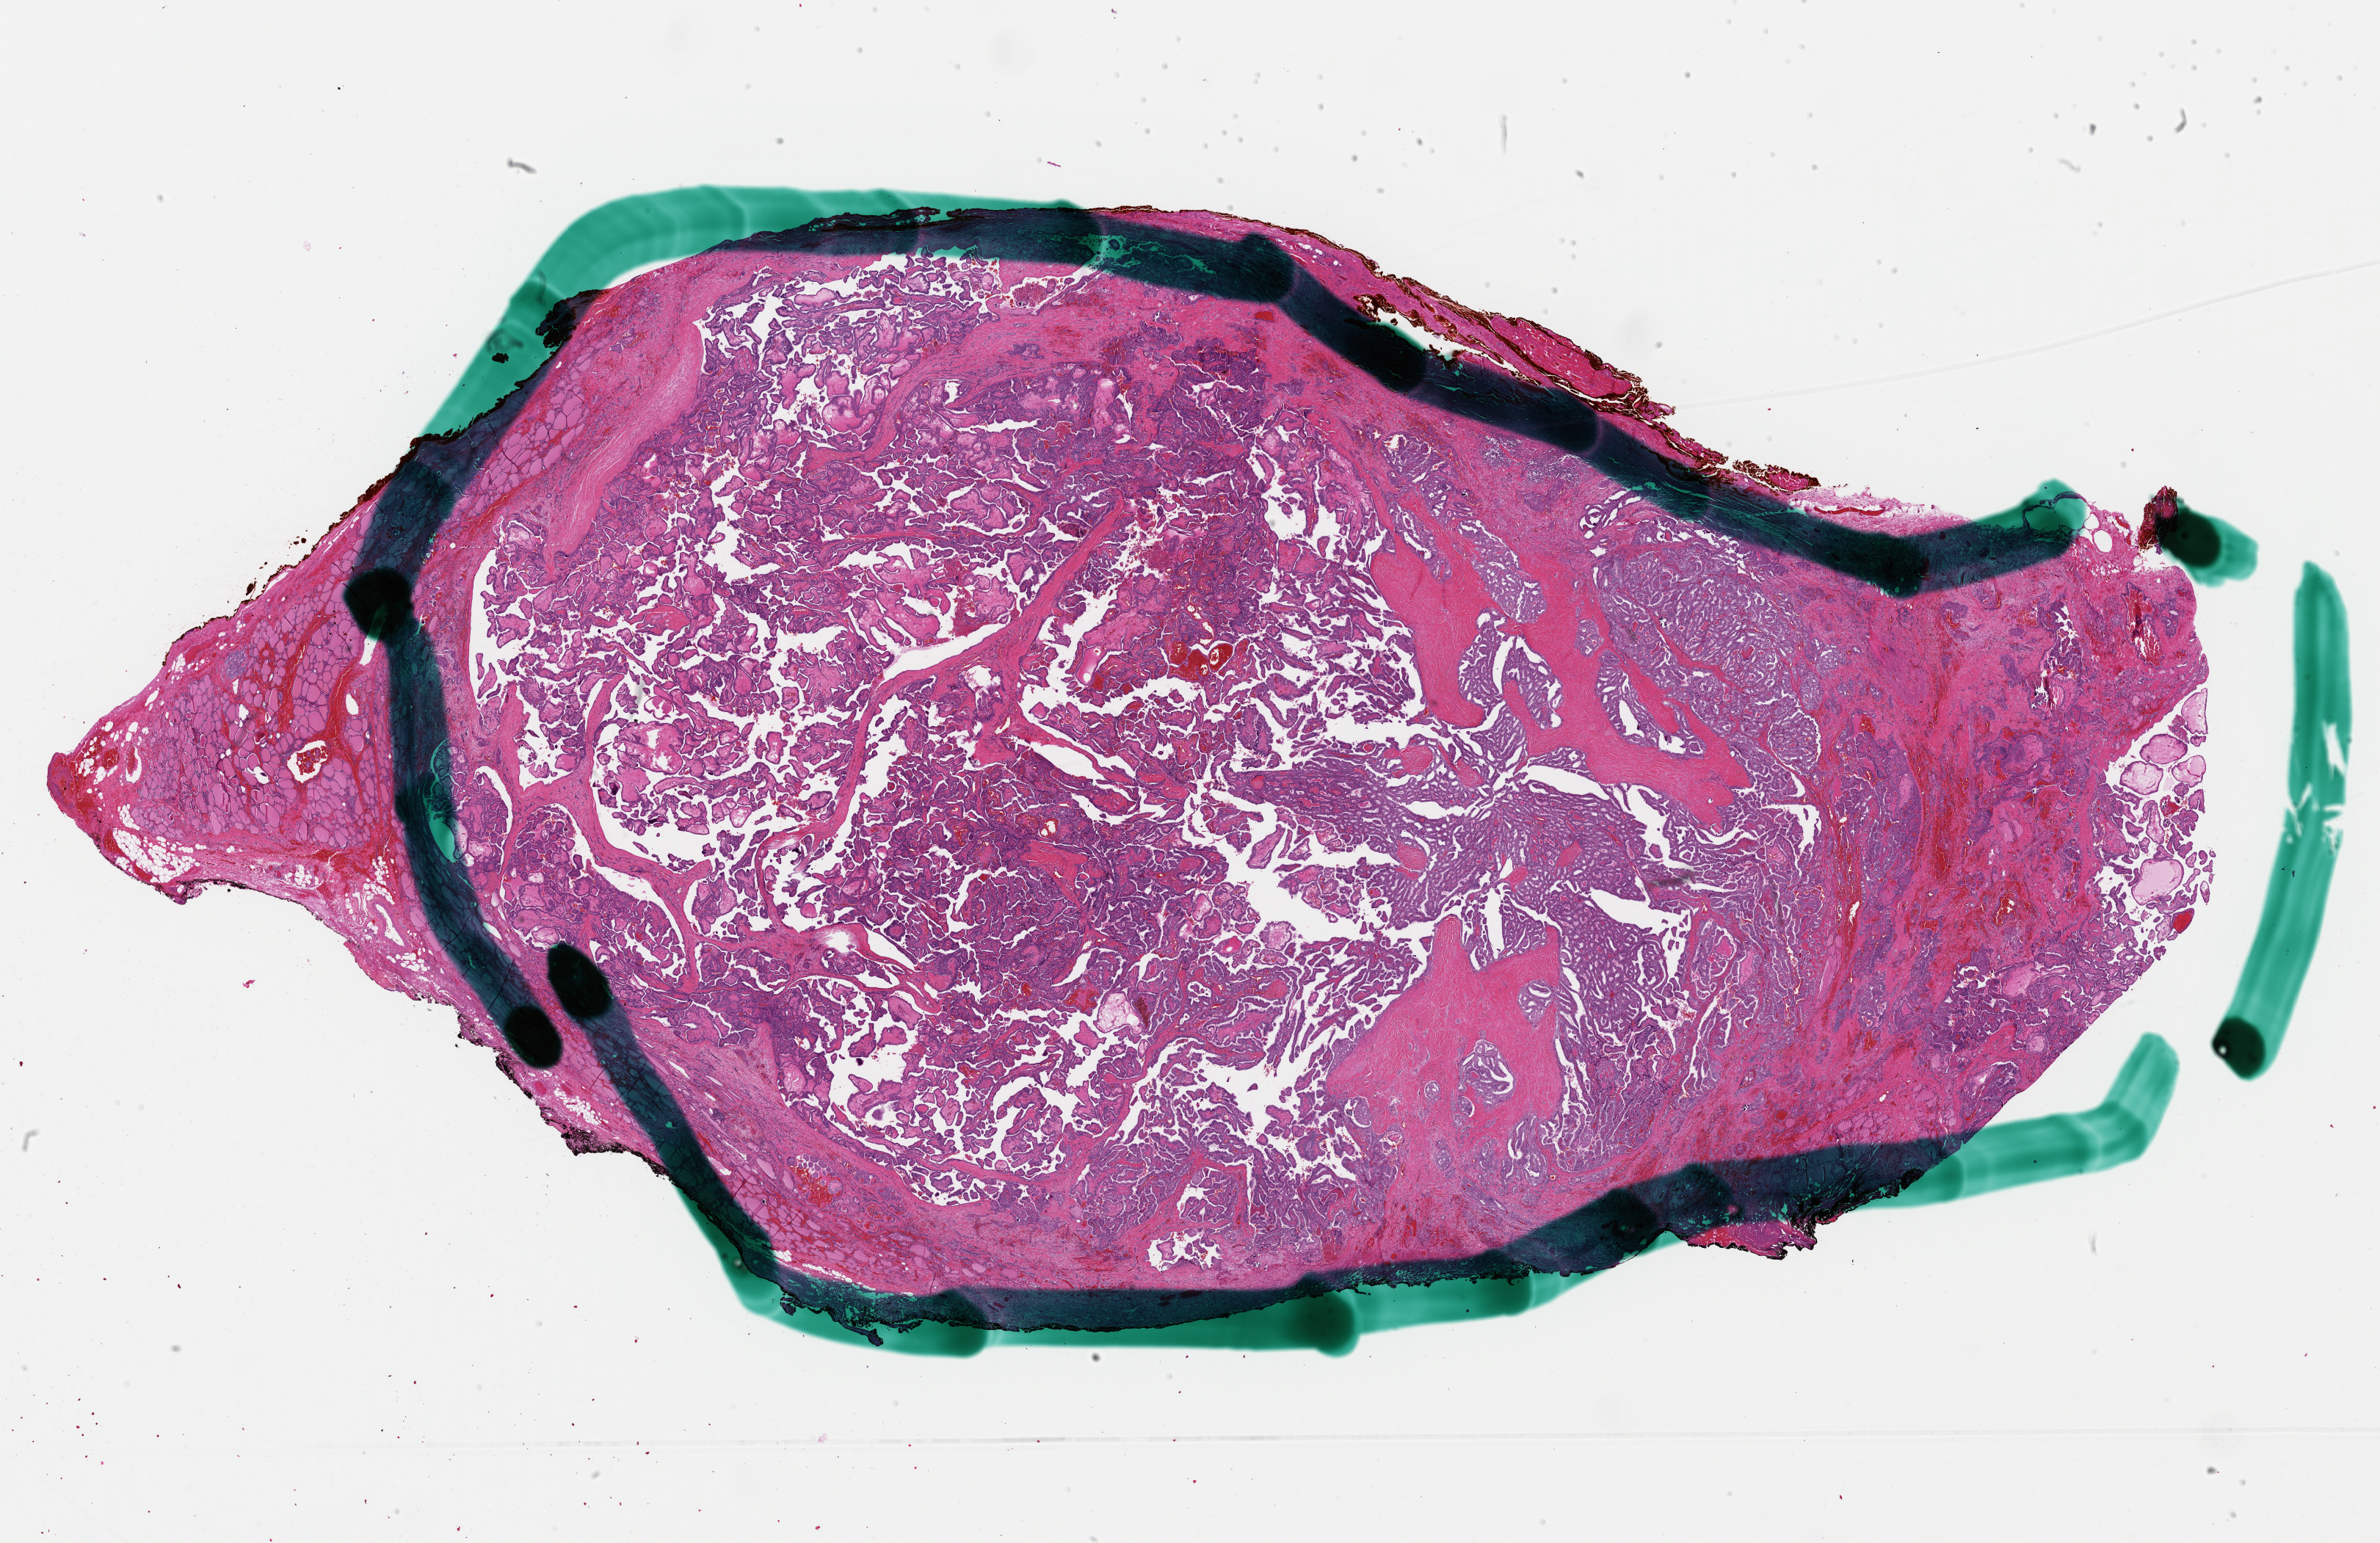
Digitized H&E-stained tissue section (whole slide) — shown as a low-resolution overview of the whole scanned area (about 25.6 x 16.6 mm, from a 40x scan). FFPE section. Sample: primary tumour, thyroid. Patient: female, age at initial diagnosis 31 years.
Laterality: bilateral. AJCC pathologic stage: I. Pathologic diagnosis: Papillary adenocarcinoma, NOS (thyroid gland).